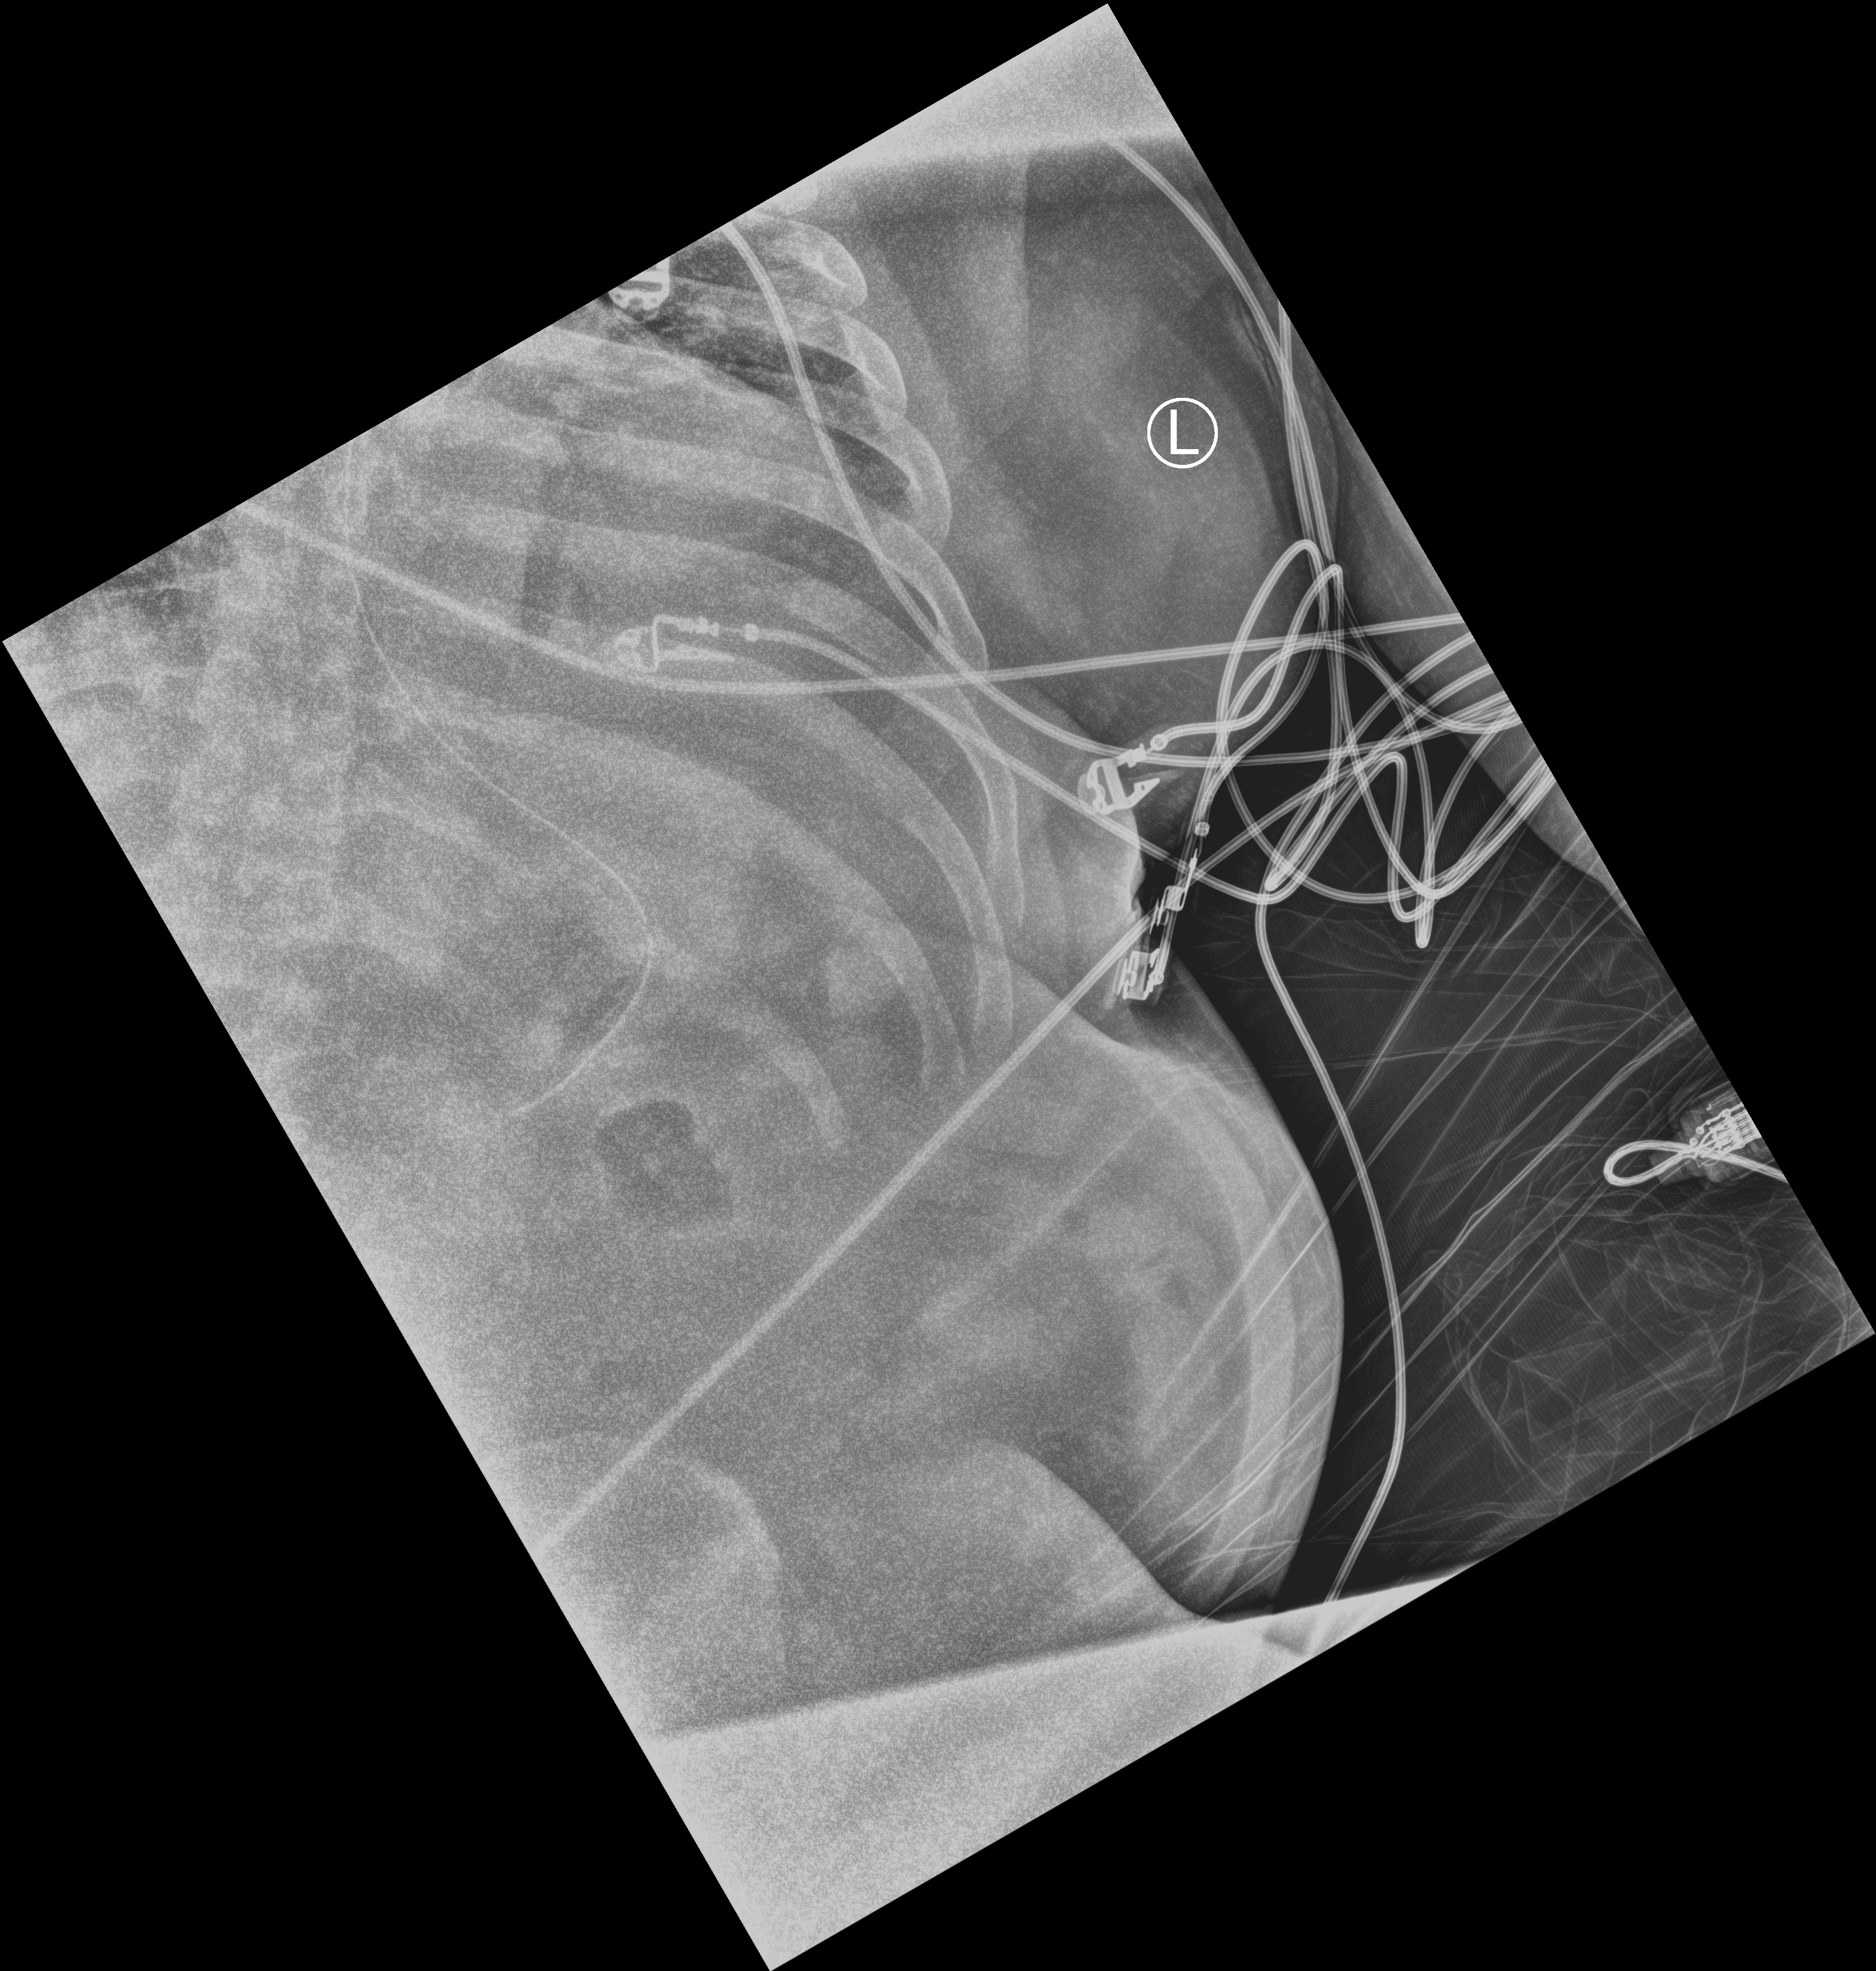
Portable chest radiograph, anteroposterior (AP) projection. Patient hospitalised with COVID-19; male, aged 18–59 years.
Hospital-stay facts (about this admission, not read from this image; timing relative to this image not recorded): admitted to intensive care during this hospital stay: yes; other chronic lung disease (admission record): no.